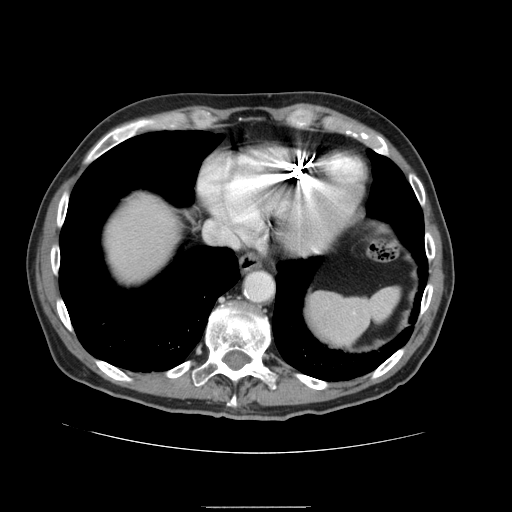
Contrast-enhanced abdominal CT, one axial slice. Position 136 of 168 along the scan axis. Intravenous contrast given. Soft-tissue window (W 400 / L 40 HU). 512 × 512 image matrix, field of view 386 × 386 mm. Male patient, age 74 years. From the clinical record (not read from this slice): diagnosis: colorectal cancer liver metastases, imaged before liver resection; multiple liver metastases: no; largest metastasis: 14.5 cm; chemotherapy before resection: no.
Annotated regions visible in this slice (manually delineated by an expert):
- liver: bounding box [x1, y1, x2, y2] px = [101, 192, 181, 286]
- planned liver remnant (the part of the liver to remain after resection): [101, 191, 185, 290]